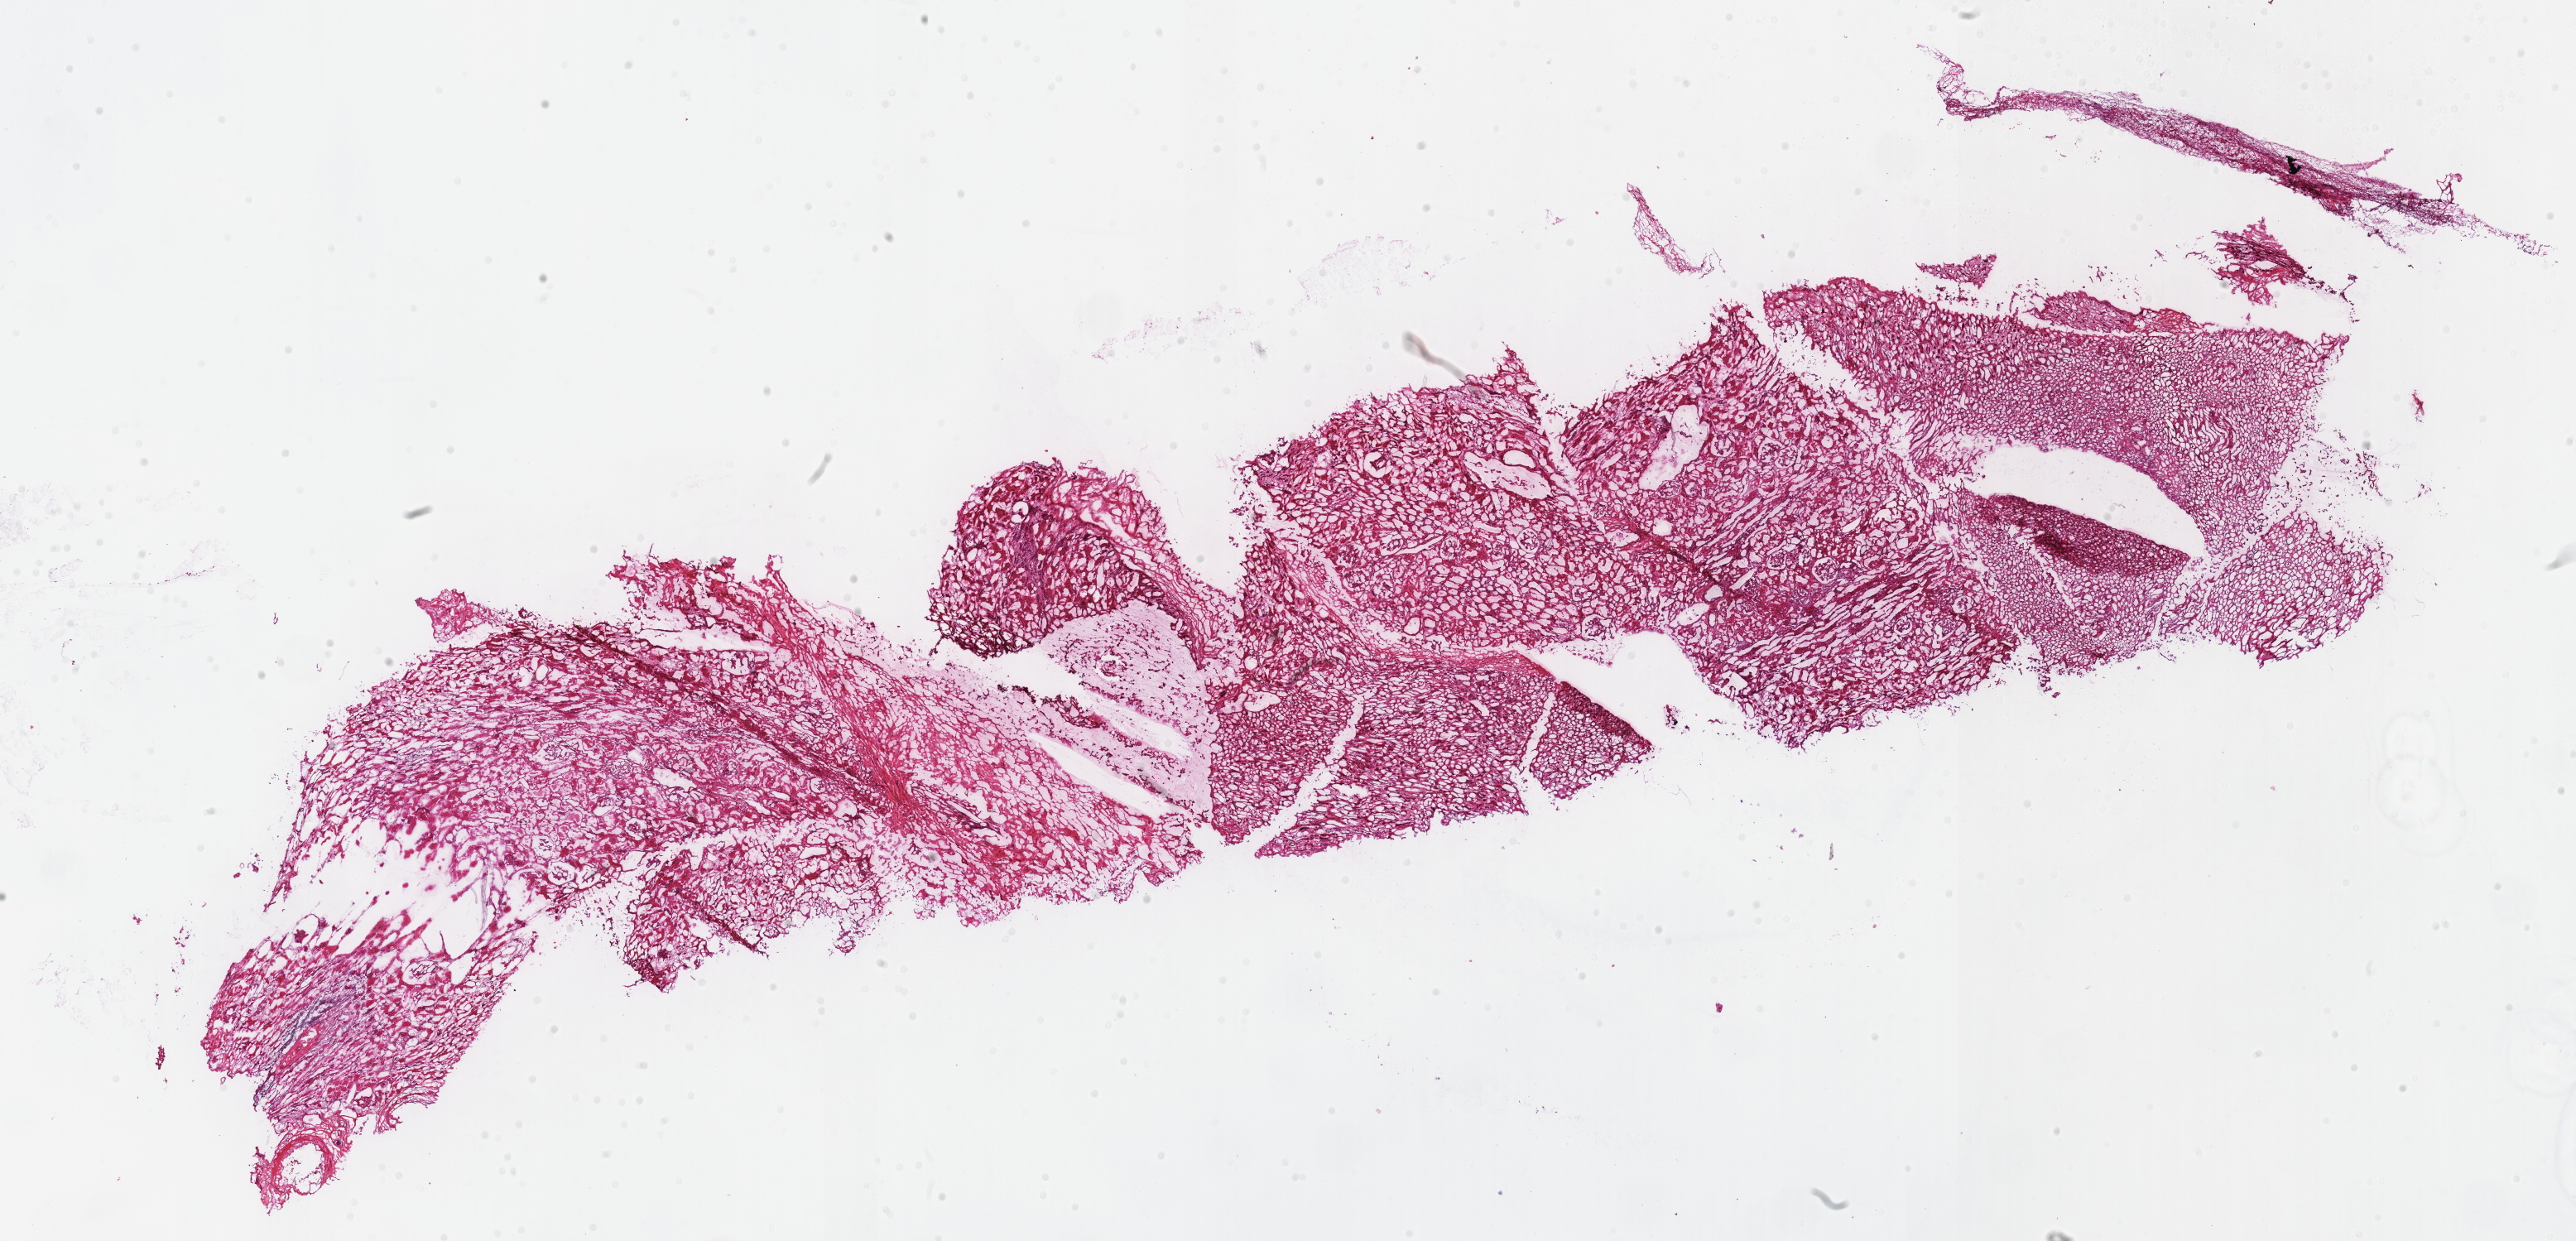
H&E whole-slide image, a low-resolution overview of the entire scanned area, about 24.5 x 11.8 mm (acquisition: 40x scan). Frozen section from the top of the tissue portion. Sample: solid tissue normal (non-tumour tissue), kidney. Male patient; age at initial diagnosis 47 years.
This section: solid tissue normal (non-tumour) sample from the same patient. Patient diagnosis: Renal cell carcinoma, chromophobe type.